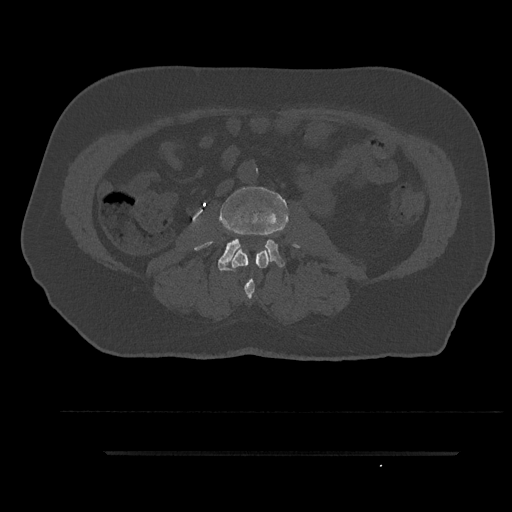
CT including the spine, one axial slice; position 69 of 797 along the scan axis; reconstruction kernel Br40s/3; 120 kVp; bone window (W 1800 / L 400 HU); 0.5 mm slice thickness; 512 × 512 image matrix, field of view 432 × 432 mm. Patient: male, 63 years. From the clinical record (not read from this slice): primary cancer: renal; vertebrae with lytic lesions (as recorded): T8.
Structures marked on this image (semi-automatically segmented with operator editing):
- L2 vertebra: box from (x=232, y=250) to (x=268, y=300) px
- L3 vertebra: (x=195, y=185)–(x=299, y=271)